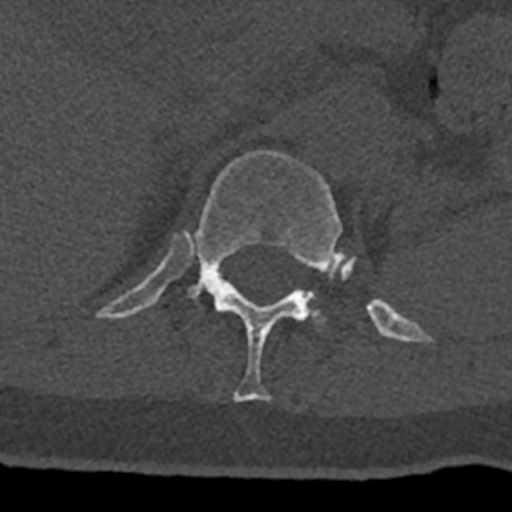
CT including the spine, one axial slice. Position 489 of 797 along the scan axis. Reconstruction kernel Br40s/3. Bone window (W 1800 / L 400 HU). 0.5 mm slice thickness. 512 × 512 image matrix, field of view 160 × 160 mm. Patient: male, 74 years. From the clinical record (not read from this slice): primary cancer: renal; vertebrae with lytic lesions (as recorded): T10, L1, L2, L3, L4, L5.
Outlined on this slice (semi-automatically segmented with operator editing):
- L1 vertebra: bounding box (x1, y1, x2, y2) in pixels: (307, 296, 326, 325)
- T12 vertebra: (96, 150, 431, 402)